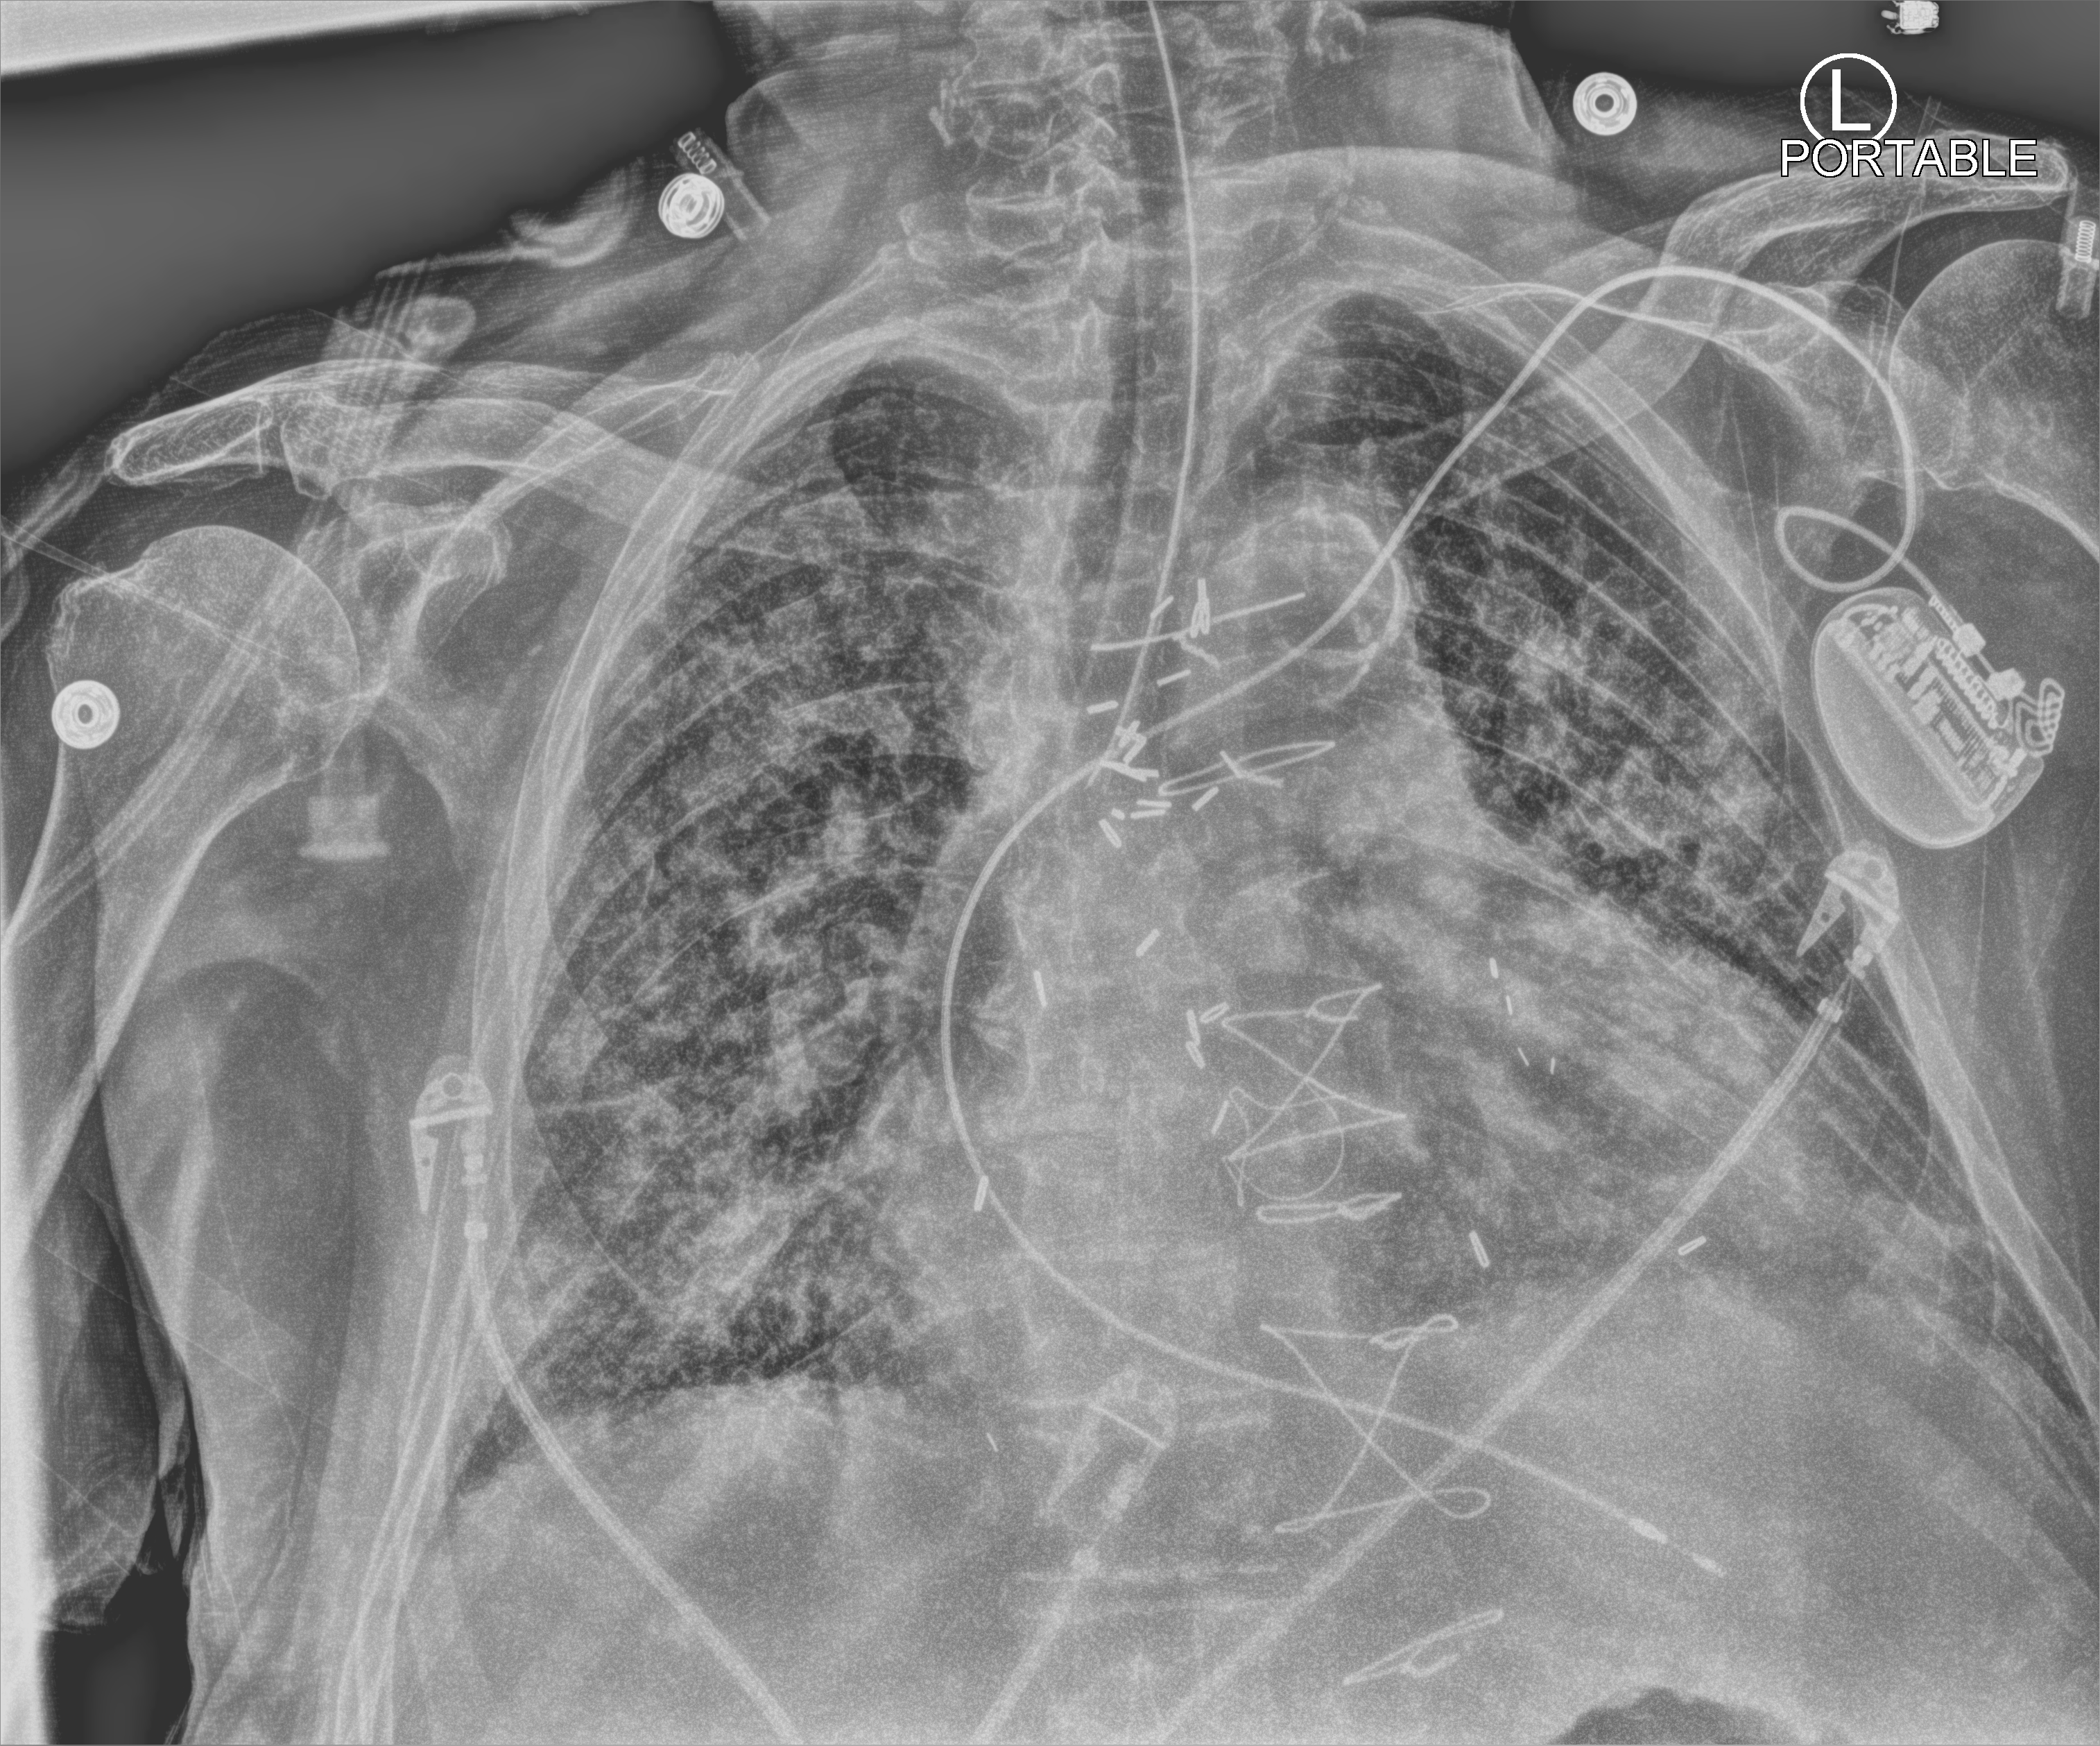
Chest X-ray (portable); anteroposterior (AP) projection. Patient hospitalised with COVID-19; male, aged 75–90 years.
From the hospital-stay record, not from the radiograph (when in the stay this image was taken is not recorded):
- diabetes (admission record): yes
- admitted to intensive care during this hospital stay: yes
- mechanically ventilated during this hospital stay: yes